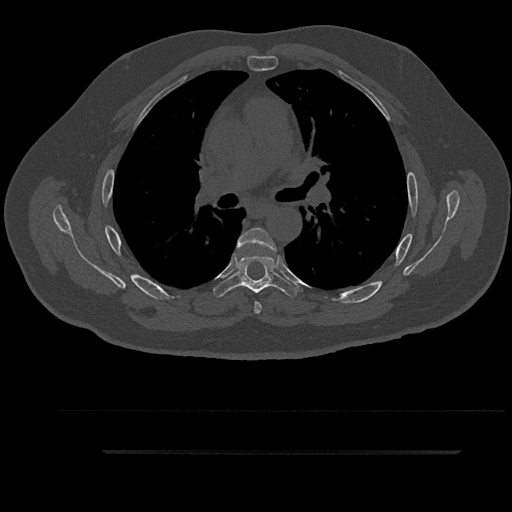
CT including the spine, one axial slice; position 595 of 797 along the scan axis; bone window (W 1800 / L 400 HU); 512 × 512 image matrix. Patient: male, 63 years. Case-level facts recorded for this patient, not image findings: primary cancer: renal.
Structures marked on this image (semi-automatic segmentation, software-assisted and operator-edited):
- T5 vertebra: bounding box <237,227,276,314> (left, top, right, bottom; pixels)
- T6 vertebra: <214,255,300,297>